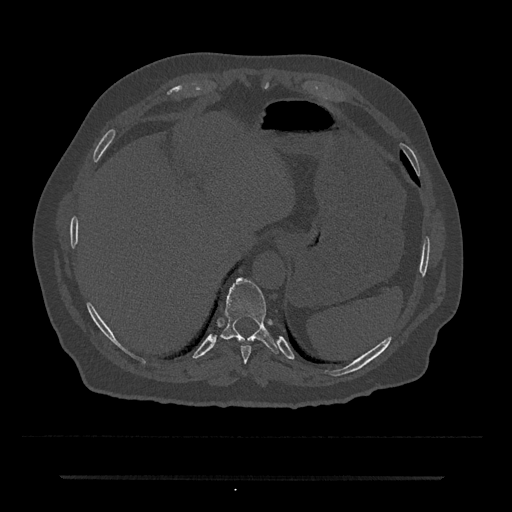
CT including the spine, one axial slice. Position 242 of 797 along the scan axis. Reconstruction kernel Br40s/3. 120 kVp. Bone window (W 1800 / L 400 HU). 512 × 512 image matrix, field of view 437 × 437 mm. Patient: male, 69 years. Case-level facts recorded for this patient, not image findings: primary cancer: prostate.
Annotated regions visible in this slice (semi-automatically segmented with operator editing):
- T10 vertebra: bounding box <221,278,279,354> (left, top, right, bottom; pixels)
- T9 vertebra: <240,345,252,364>